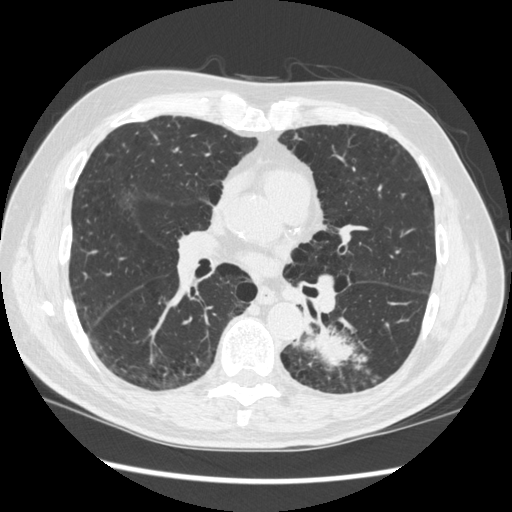
Low-dose screening chest CT, one axial slice. Position 166 of 348 along the scan axis. Reconstruction kernel STANDARD. 120 kVp. Lung window (W 1500 / L -600 HU). 1.25 mm slice thickness. 512 × 512 image matrix.
Structures marked on this image (expert manual segmentation):
- lesion 1 (tumor, lower lobe of left lung): box from (x=301, y=328) to (x=367, y=374) px